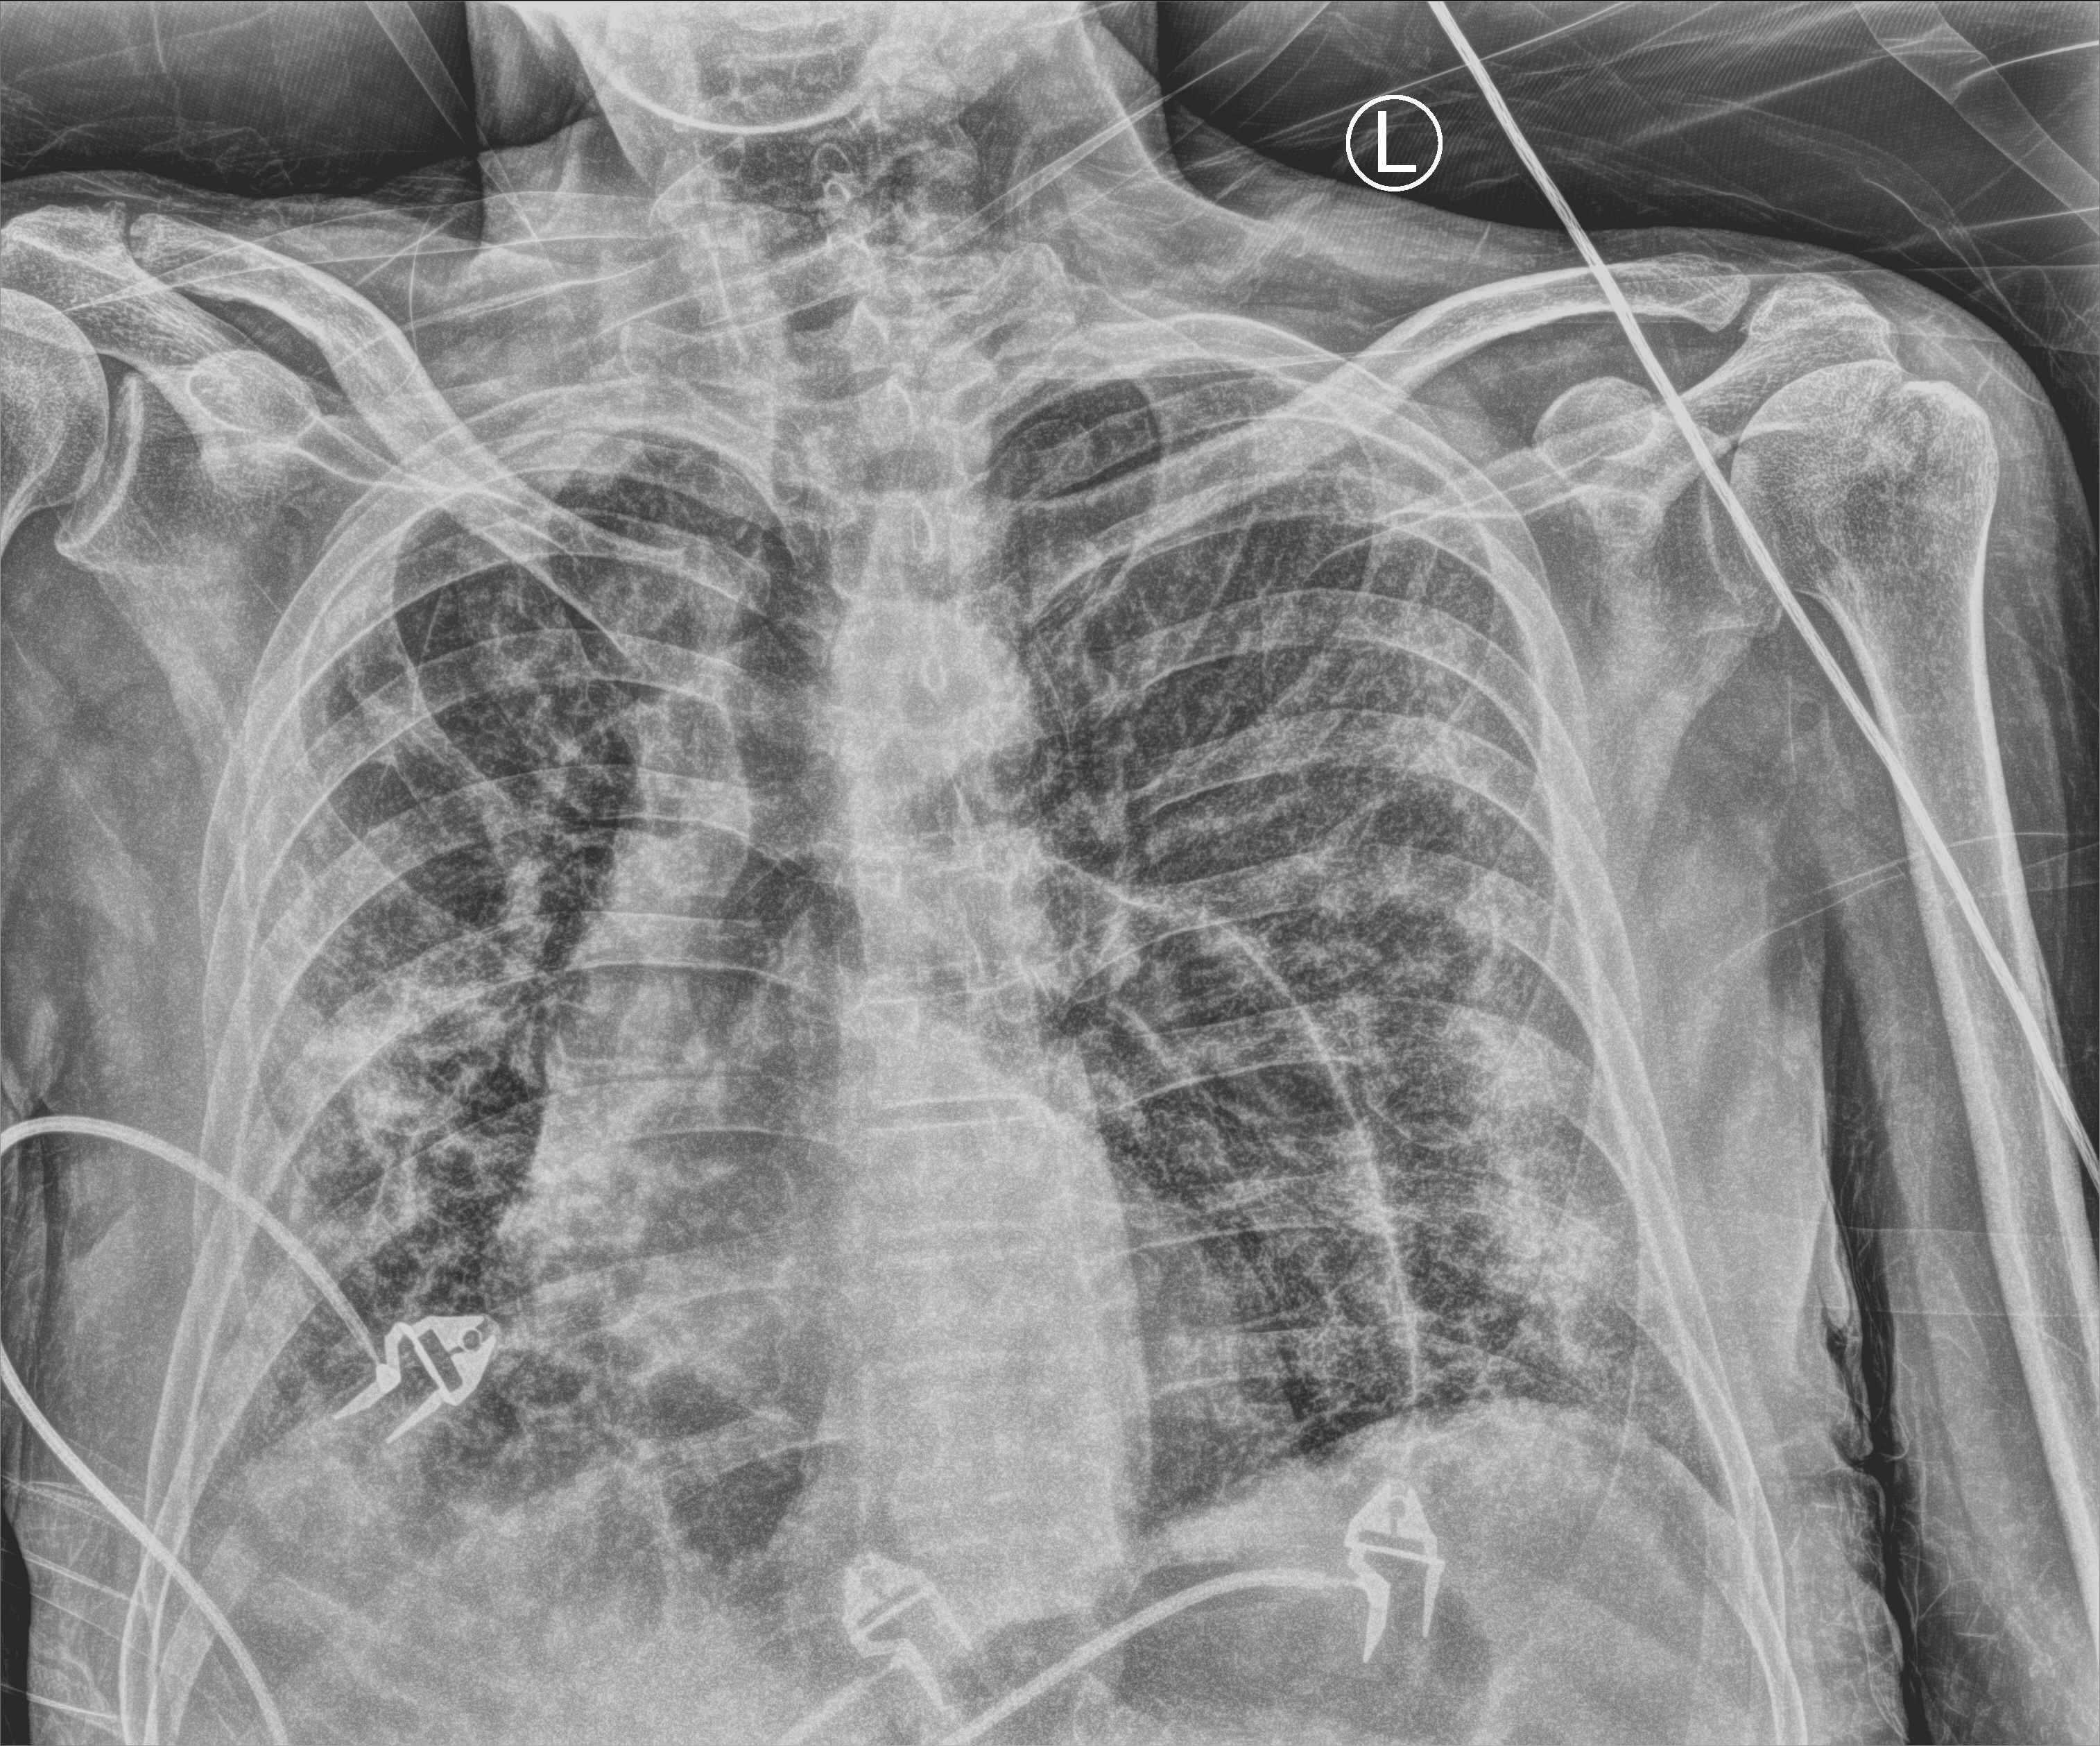
Chest X-ray (portable). Patient hospitalised with COVID-19; male, aged 60–74 years.
From the hospital-stay record, not from the radiograph (when in the stay this image was taken is not recorded):
- admitted to intensive care during this hospital stay: no
- mechanically ventilated during this hospital stay: no